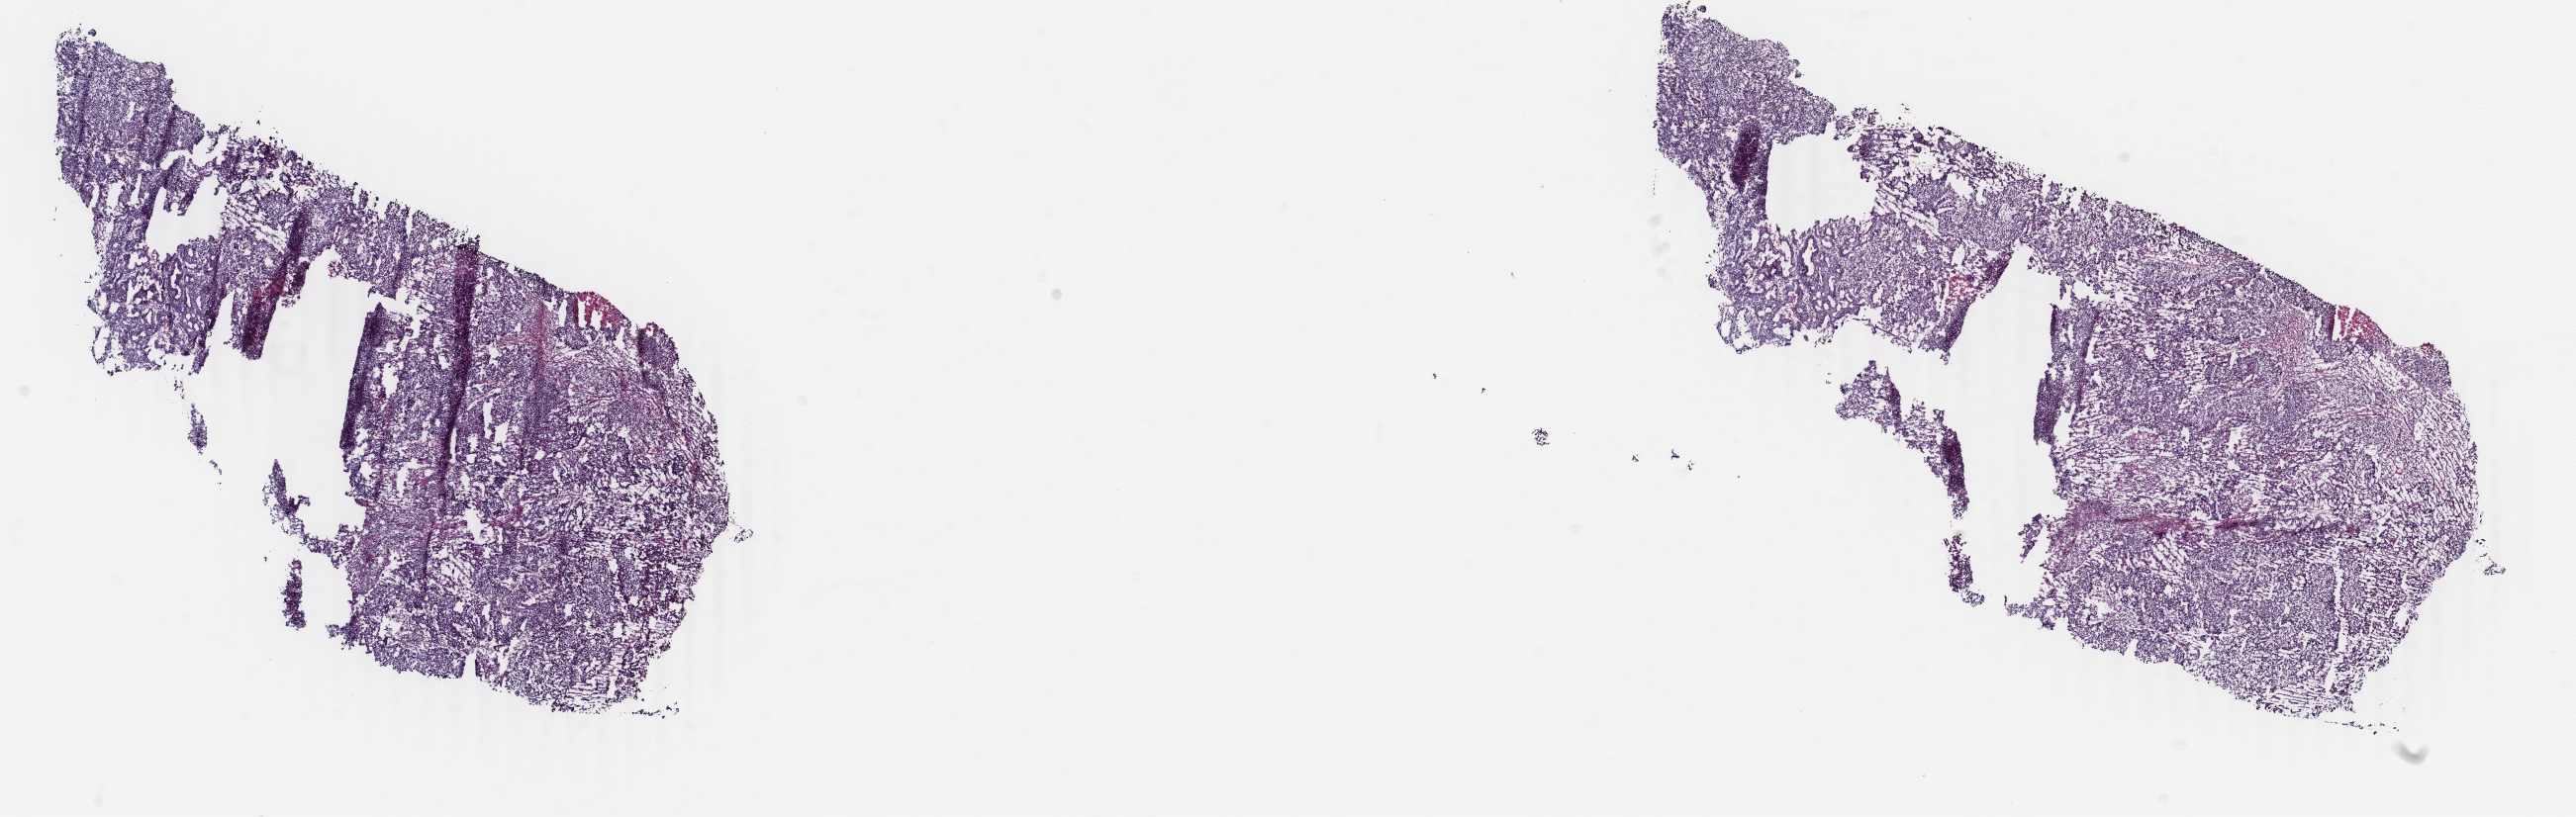
Whole-slide histology image, Hematoxylin and eosin (H&E) stained, whole scanned area (about 20.7 x 6.6 mm) shown as a low-resolution overview; frozen section; uterus, primary tumour sample. Female, age 53 years at initial diagnosis. Histologic grade: G3 (poorly differentiated). Pathologist review of this section (percent, as recorded): tumour cells 96%, tumour nuclei 96%, normal cells 0%, stromal cells 1%, necrosis 3%. Inflammatory infiltration, as recorded: lymphocyte infiltration 4%, monocyte infiltration 0%, neutrophil infiltration 1%.
FIGO stage: IB. Lymph nodes positive (case pathology): 0 of 4 examined. Pathologic diagnosis: Endometrioid adenocarcinoma, NOS.